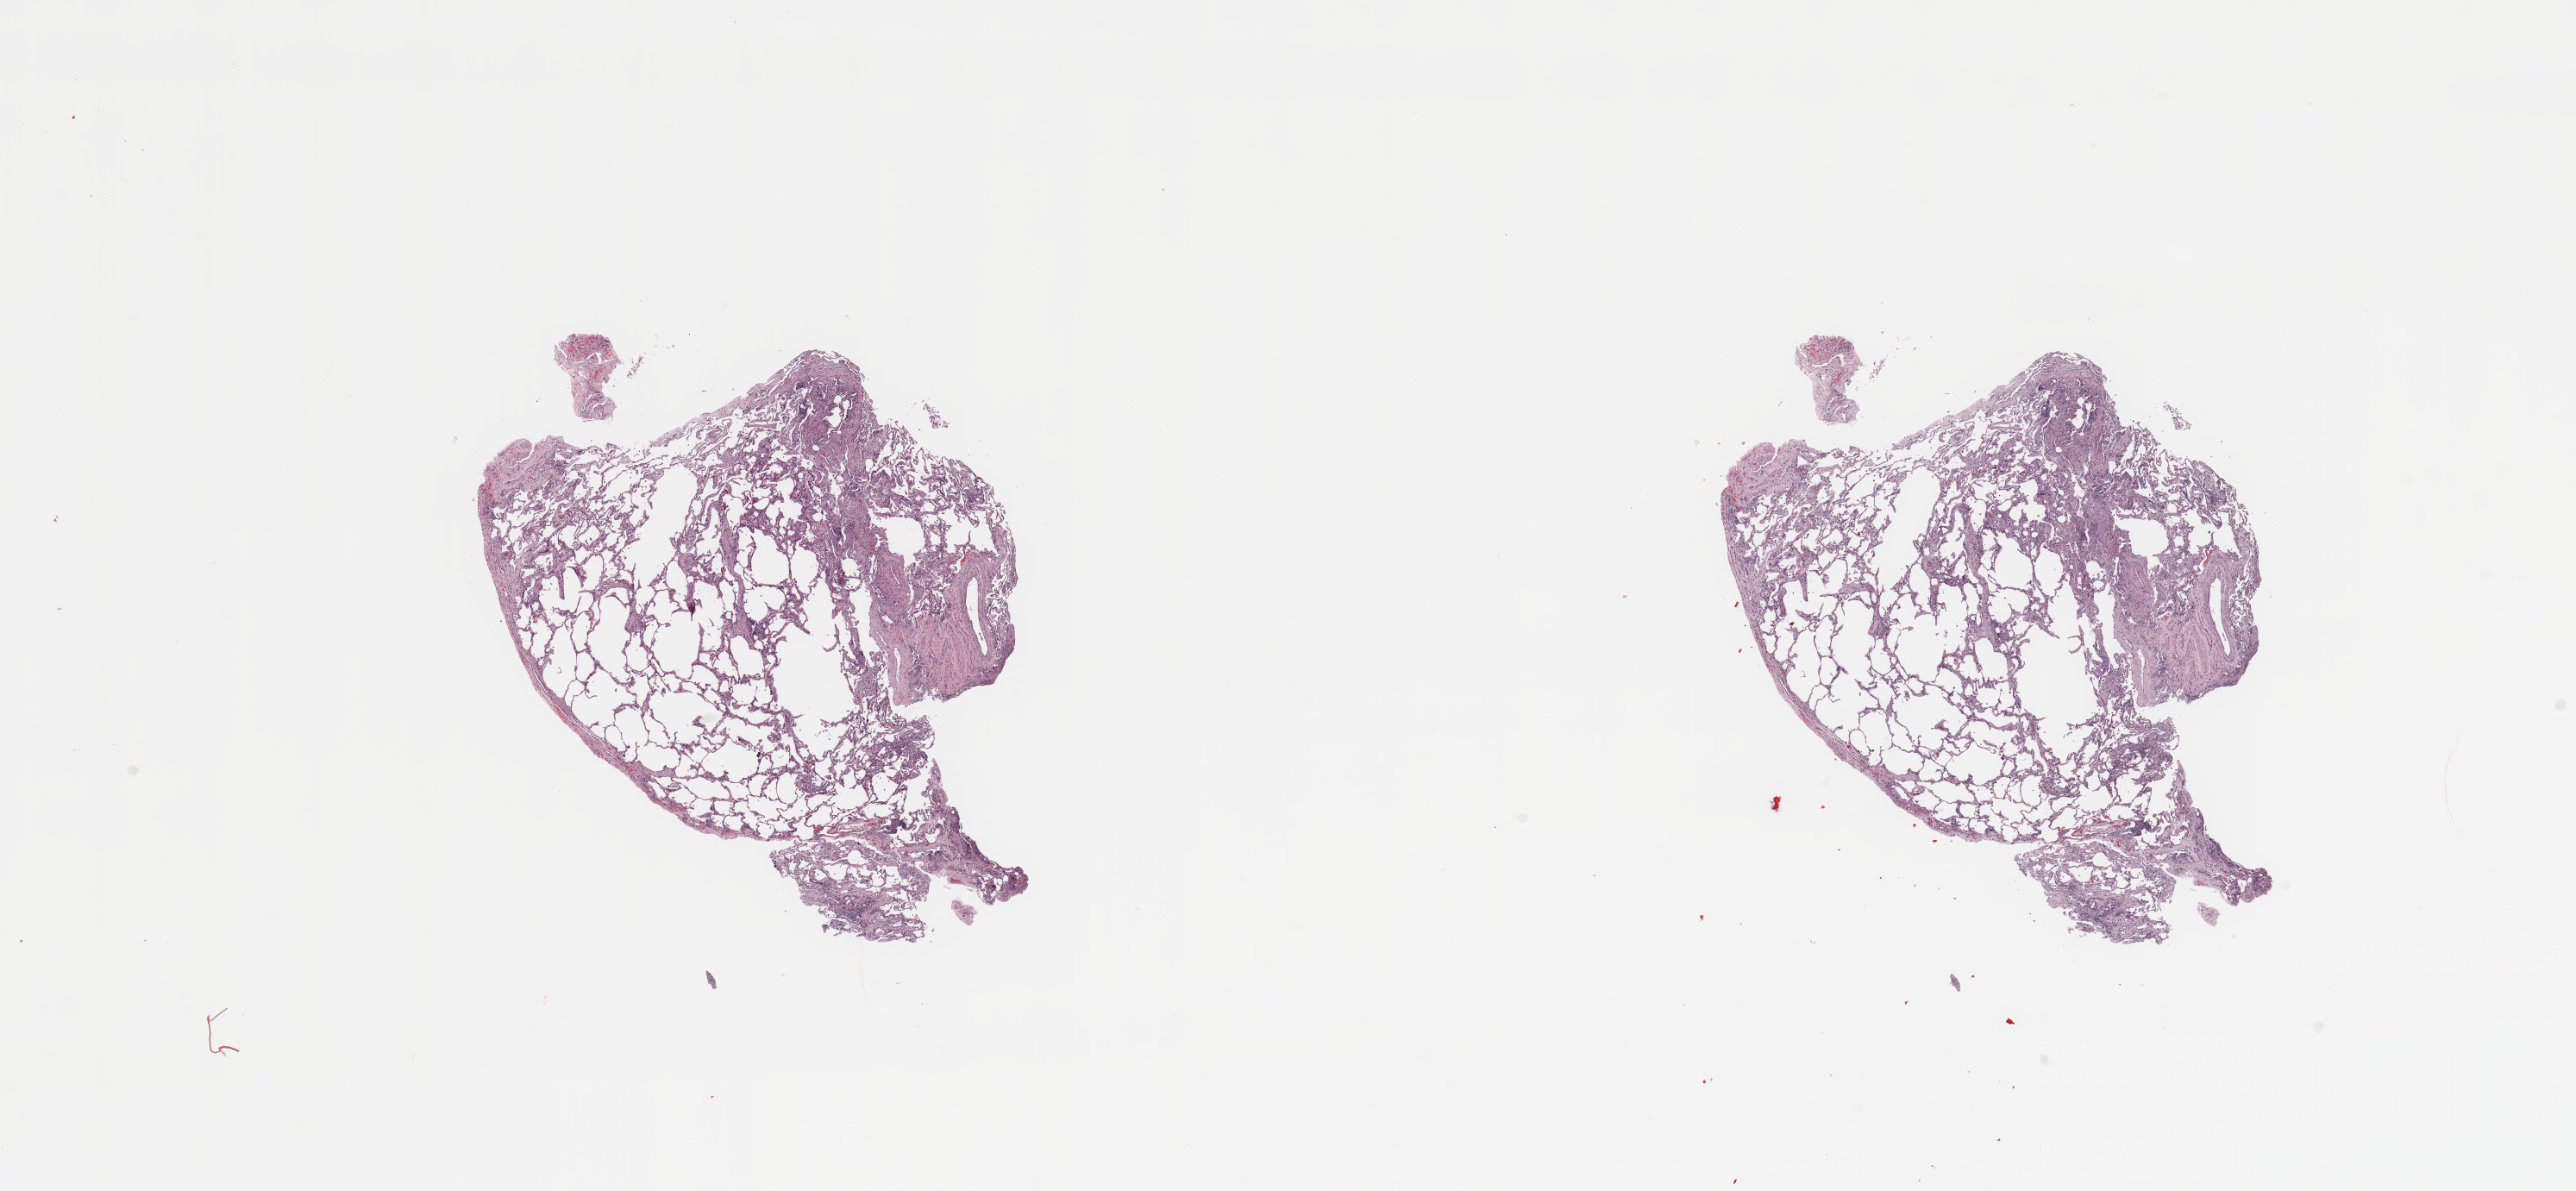
Digitized H&E-stained tissue section (whole slide) — low-resolution overview of the scanned area, about 23.6 x 10.9 mm (slide scanned at 20x); normal (non-tumour) tissue sample, sampled site: lung. 79-year-old female patient.
This section: normal (non-tumour) tissue from the same patient. Patient diagnosis: Adenocarcinoma, NOS.